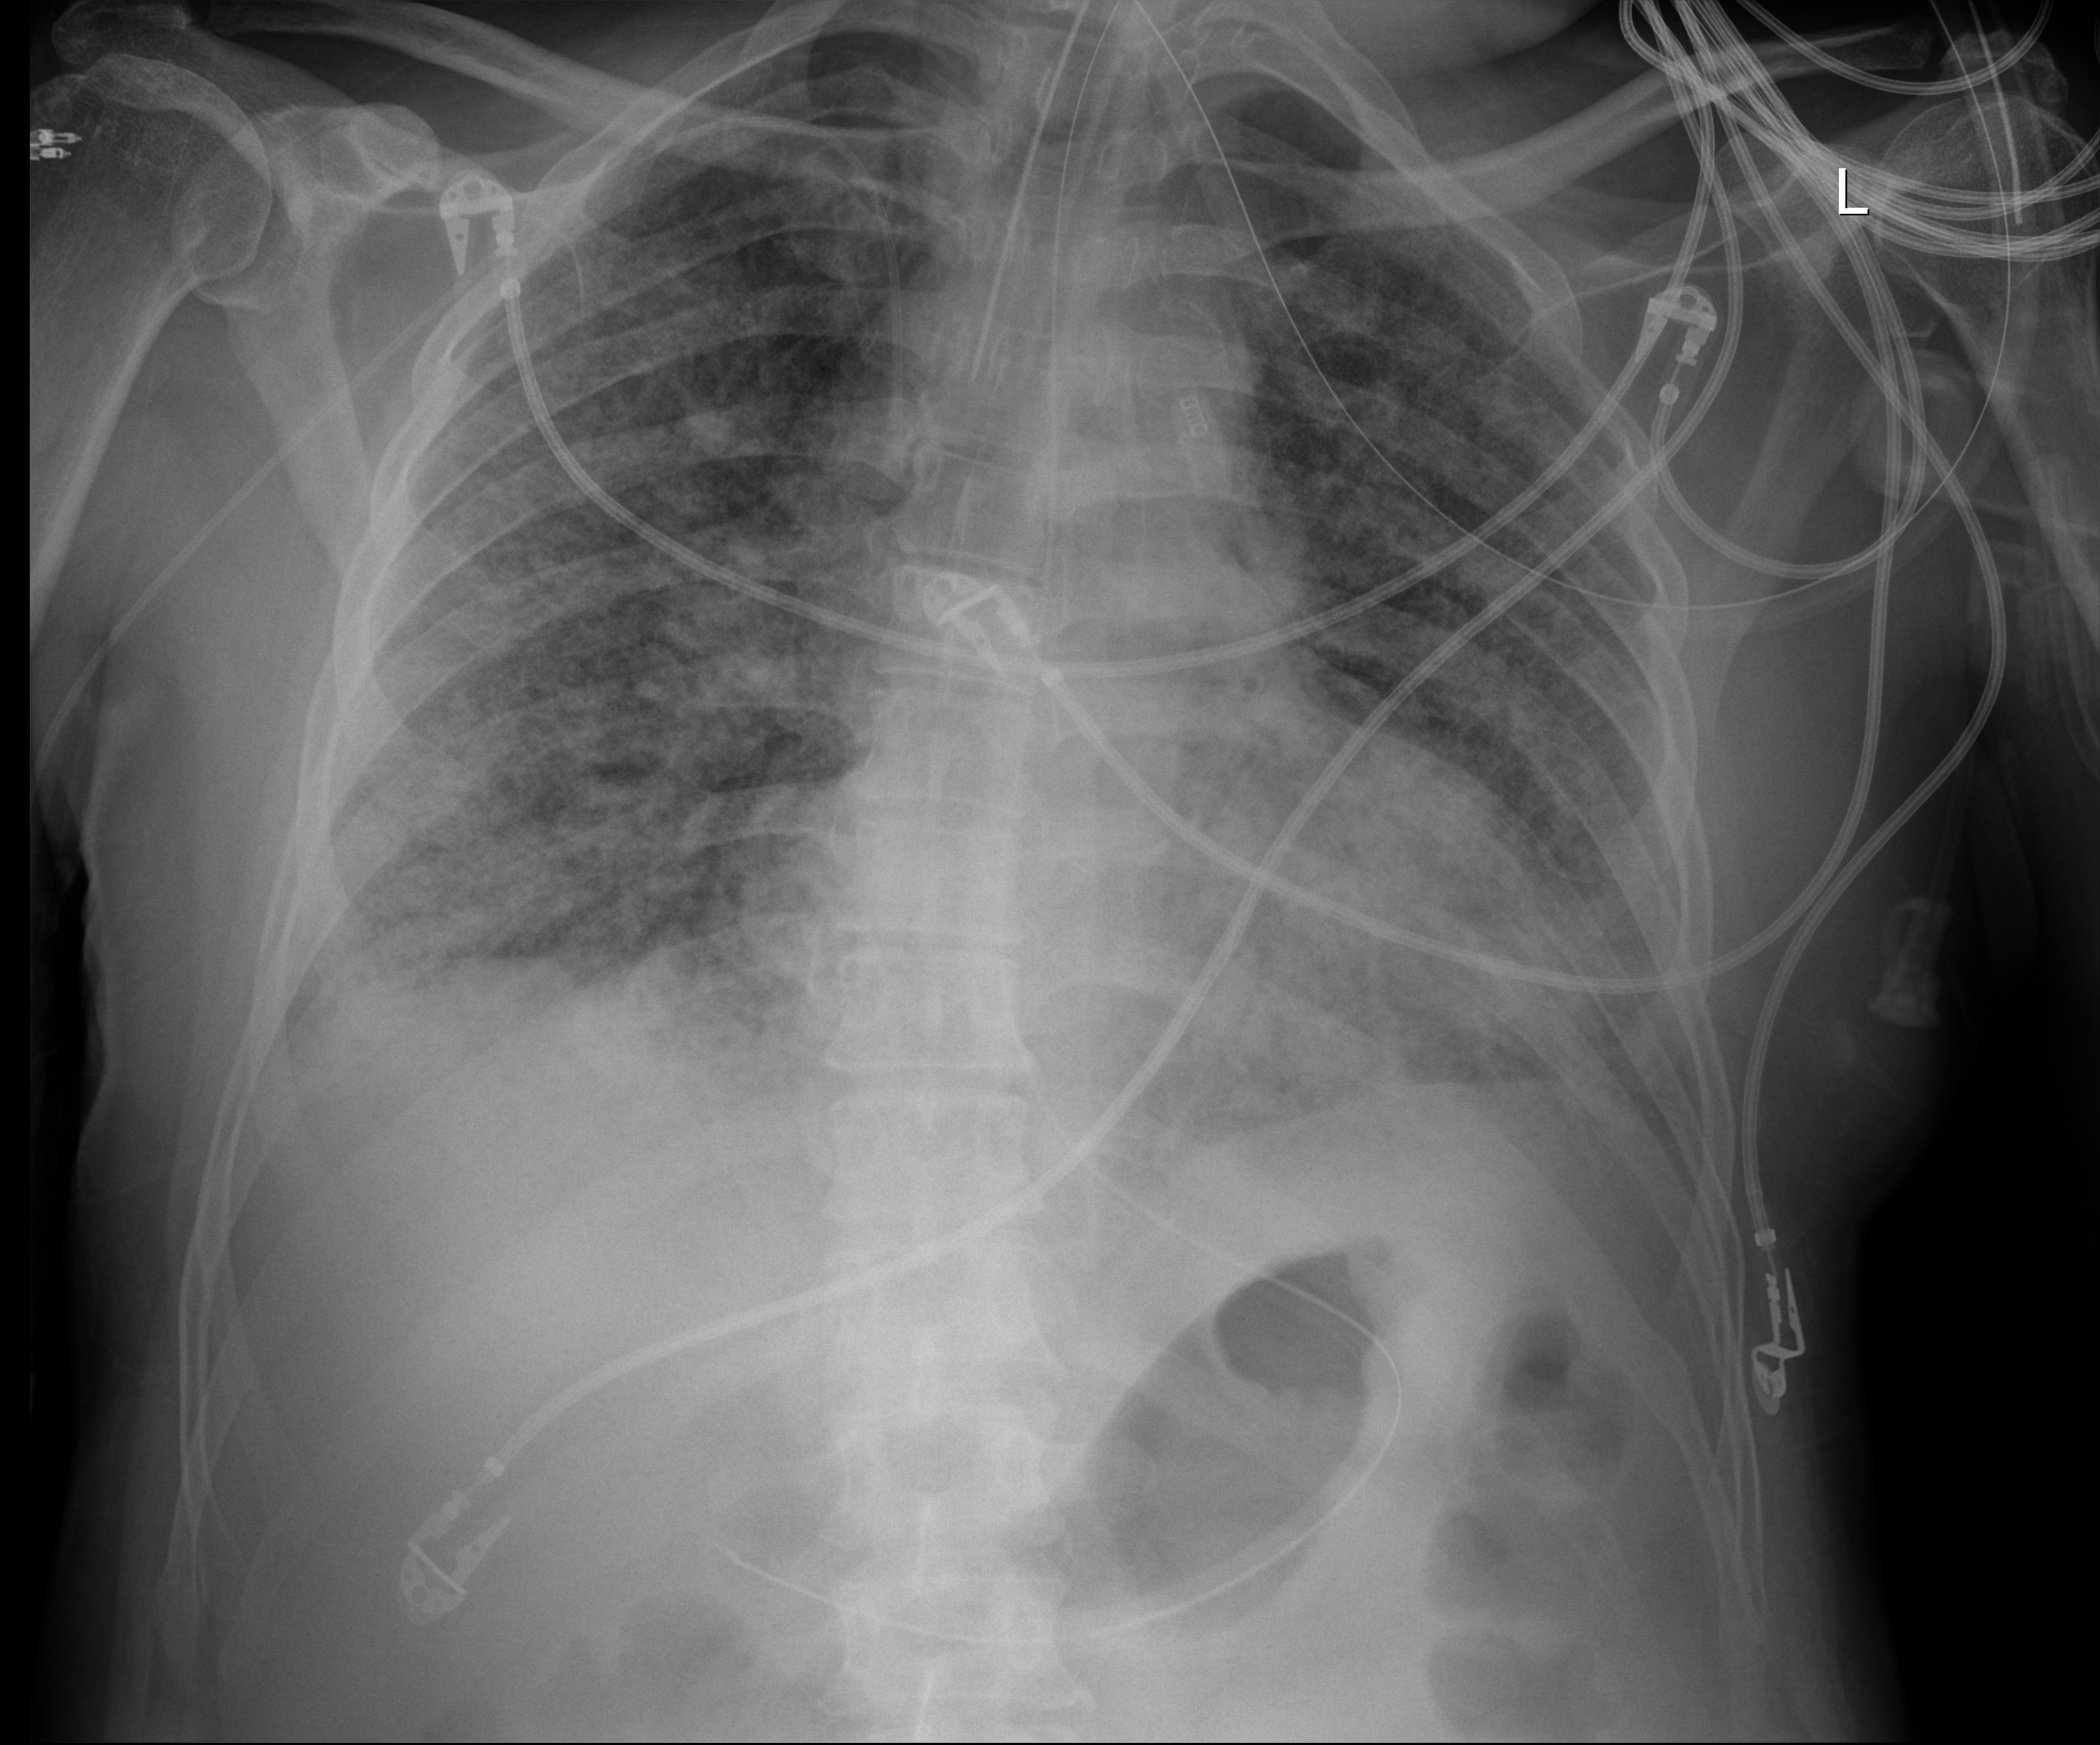
Chest X-ray (portable), anteroposterior (AP) projection. Male patient hospitalised with COVID-19, age 60–74 years.
From the hospital-stay record, not from the radiograph (when in the stay this image was taken is not recorded):
- mechanically ventilated during this hospital stay: yes
- COPD (admission record): no
- other chronic lung disease (admission record): yes